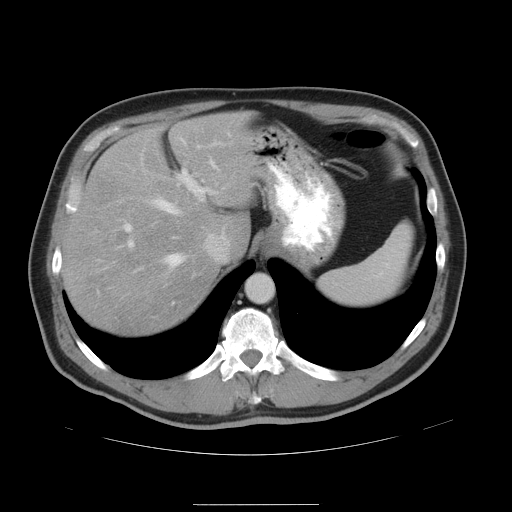
Contrast-enhanced abdominal CT, one axial slice; slice 36 of 47 in the series (ordered by position); 120 kVp; intravenous contrast given; soft-tissue window (W 400 / L 40 HU); 5 mm slice thickness; 512 × 512 image matrix, field of view 420 × 420 mm. Male patient, age 61 years. From the clinical record (not read from this slice): diagnosis: colorectal cancer liver metastases, imaged before liver resection; multiple liver metastases: no; largest metastasis: 1.2 cm; disease in both lobes: no.
Annotated regions visible in this slice (manually delineated by an expert):
- hepatic veins: bounding box [x1, y1, x2, y2] px = [150, 138, 227, 267]
- liver: [62, 113, 252, 337]
- planned liver remnant (the part of the liver to remain after resection): [63, 113, 252, 337]
- portal vein (with intrahepatic branches): [125, 168, 214, 272]